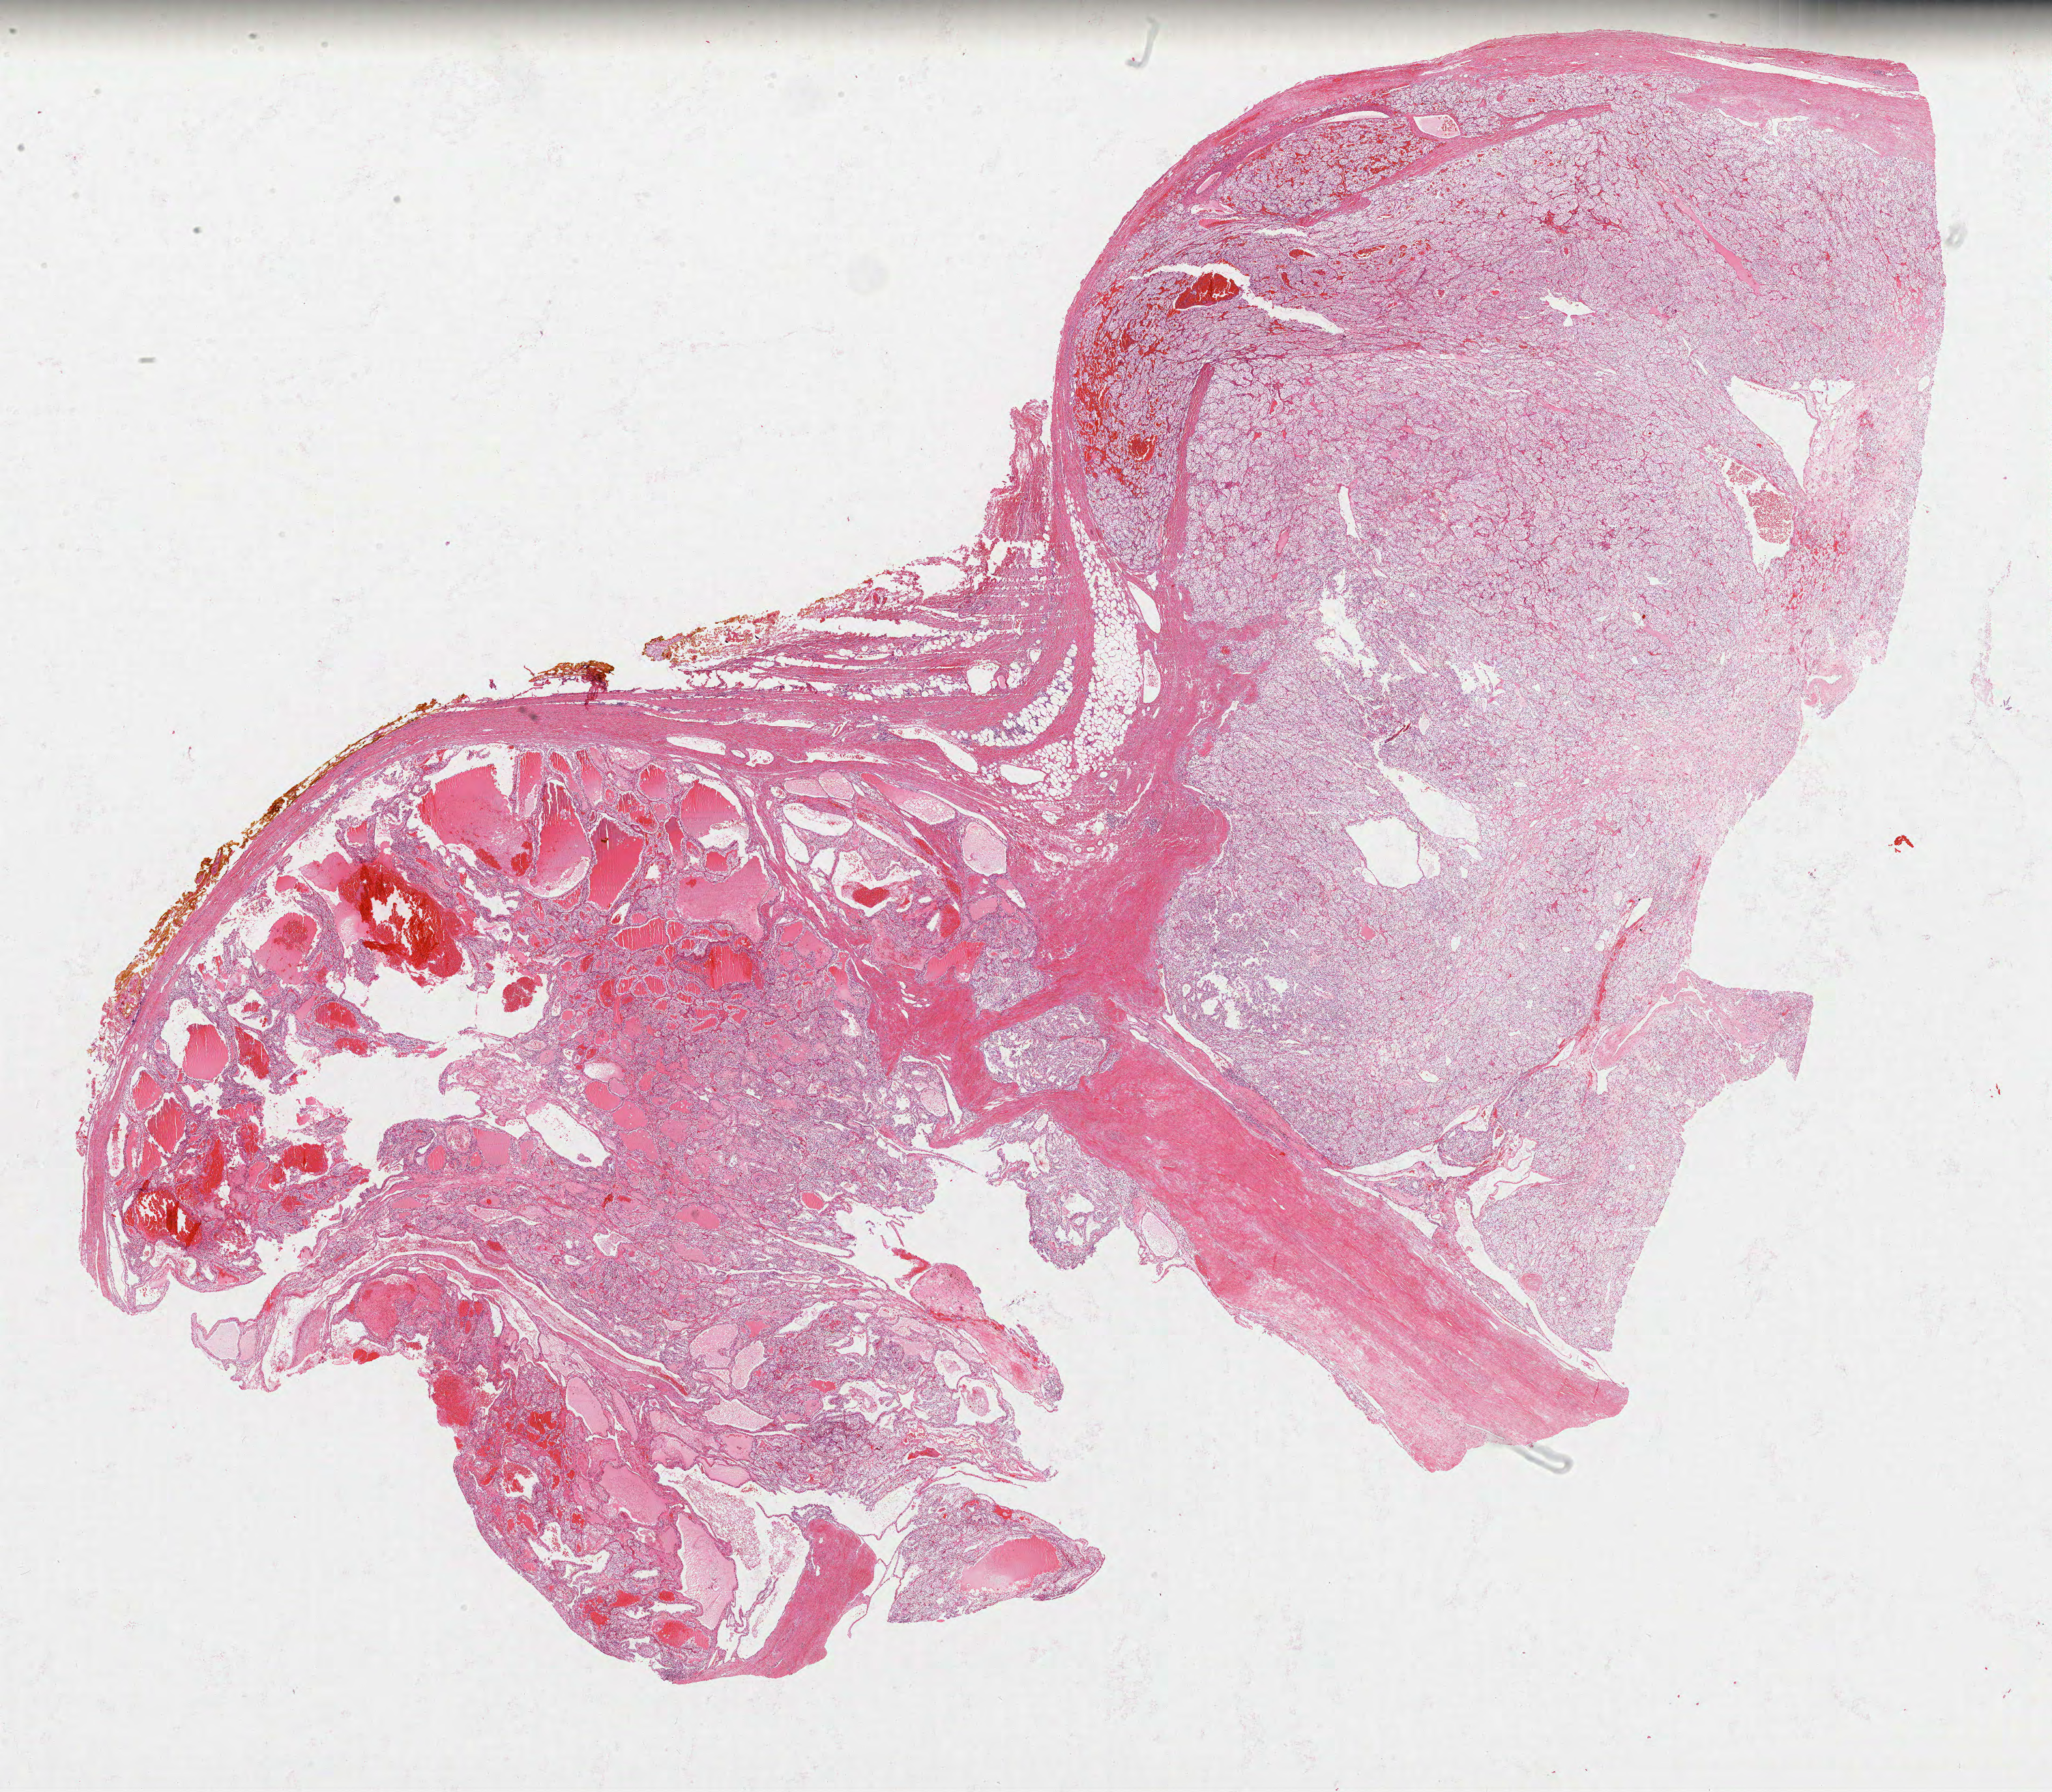
Whole-slide histology image, Hematoxylin and eosin (H&E) stained — shown as a low-resolution overview of the whole scanned area (about 25.4 x 22.2 mm, acquisition: 40x scan), formalin-fixed paraffin-embedded (FFPE) diagnostic section, primary tumour sample from the kidney. Male patient; age at initial diagnosis 67 years. Histologic grade: G2 (moderately differentiated).
• pathologic diagnosis: Clear cell adenocarcinoma, NOS
• AJCC pathologic stage: II
• laterality: left